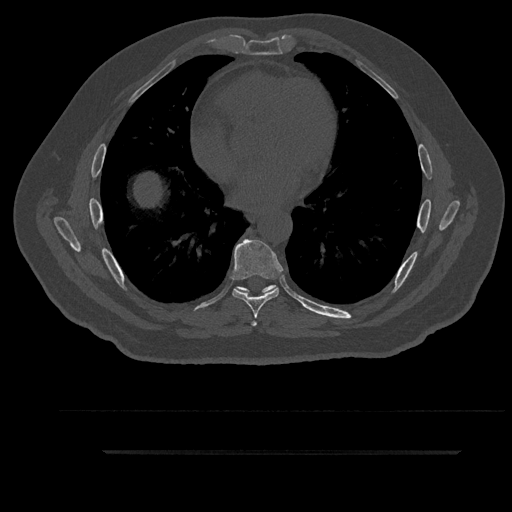
CT including the spine, one axial slice. Slice 515 of 797 in the series (ordered by position). Reconstruction kernel Br40s/3. Bone window (W 1800 / L 400 HU). 0.5 mm slice thickness. 512 × 512 image matrix. Male patient, age 63 years. From the clinical record (not read from this slice): primary cancer: renal; vertebrae with lytic lesions (as recorded): T8.
Annotated regions visible in this slice (semi-automatically segmented with operator editing):
- T6 vertebra: bounding box <235,285,275,326> (left, top, right, bottom; pixels)
- T7 vertebra: <232,239,284,318>
- T8 vertebra: <236,285,278,292>